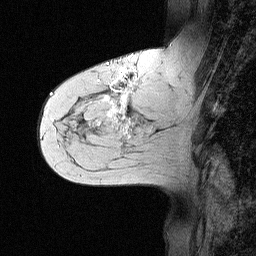
Breast MRI (dynamic contrast-enhanced), one sagittal slice. Position 23 of 64 along the scan axis. Dynamic contrast-enhanced study with each time point stored as its own series, time point 2 of 3 at this slice position (early post-contrast, ordered by acquisition time). 1.5 T. TE 4.5 ms, TR 11 ms. 2.06 mm slice thickness. 256 × 256 image matrix, field of view 200 × 200 mm. Patient: female, 55 years. Case-level facts recorded for this patient, not image findings: setting: breast cancer imaged before/during neoadjuvant chemotherapy; receptor status: triple-negative.
Outlined on this slice (semi-automatic segmentation, software-assisted and operator-edited):
- analysis volume of interest (the breast-tissue region the enhancement analysis was run in; not a lesion): bounding box <71,63,147,145> (left, top, right, bottom; pixels)
- tumour enhancement mask (voxels above the 90 % enhancement threshold inside the analysis volume of interest): <103,69,138,125>